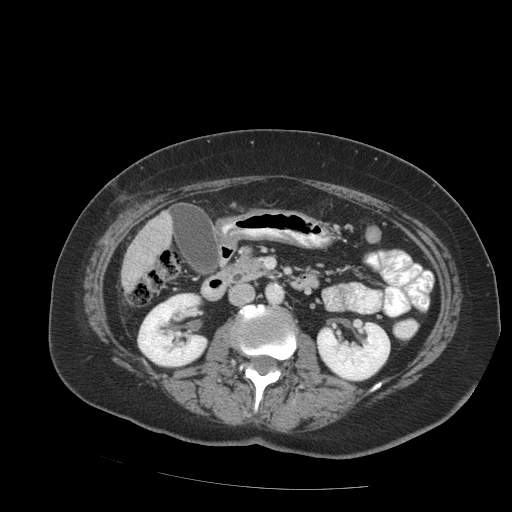
Contrast-enhanced abdominal CT (liver protocol), one axial slice. Position 28 of 99 along the scan axis. Reconstruction kernel STANDARD. 140 kVp. Soft-tissue window (W 400 / L 40 HU). 2.5 mm slice thickness. 512 × 512 image matrix, field of view 400 × 400 mm. From the clinical record (not read from this slice): diagnosis: hepatocellular carcinoma (patient treated with transarterial chemoembolisation; whether this scan precedes or follows treatment is not stated here); TNM stage (as recorded): Stage-IVB; Child-Pugh class: A; tumour differentiation: moderately differentiated; tumour nodularity: uninodular.
Annotated regions visible in this slice (semi-automatically segmented with operator editing):
- liver parenchyma outside the tumour (the mass and vessels are separate outlines, so this box may not span the whole liver): box from (x=120, y=212) to (x=172, y=292) px